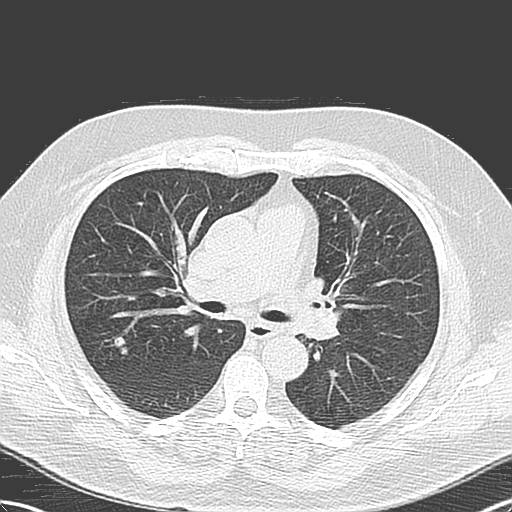
Low-dose screening chest CT, one axial slice. Position 72 of 131 along the scan axis. 120 kVp. Lung window (W 1500 / L -600 HU). 3.2 mm slice thickness. 512 × 512 image matrix.
Structures marked on this image (outlined manually by an expert reader):
- lesion 1 (tumor, upper lobe of right lung): bounding box <112,337,128,355> (left, top, right, bottom; pixels)